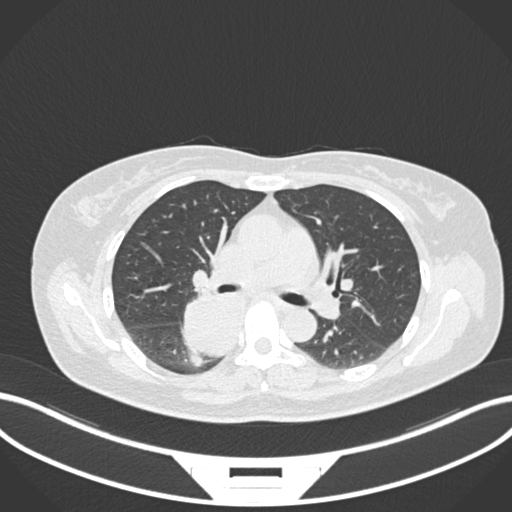
Chest CT, one axial slice; slice 611 of 677 in the series (ordered by position); reconstruction kernel B30f; lung window (W 1500 / L -600 HU); 1 mm slice thickness; 512 × 512 image matrix, field of view 400 × 400 mm. Patient: female, 54 years. Case-level facts recorded for this patient, not image findings: clinical TNM (as recorded): T4 N0 M0.
Annotated regions visible in this slice (rectangle marked by the reading radiologist):
- lung tumour (recorded histology: adenocarcinoma): bounding box (x1, y1, x2, y2) in pixels: (181, 287, 251, 361)